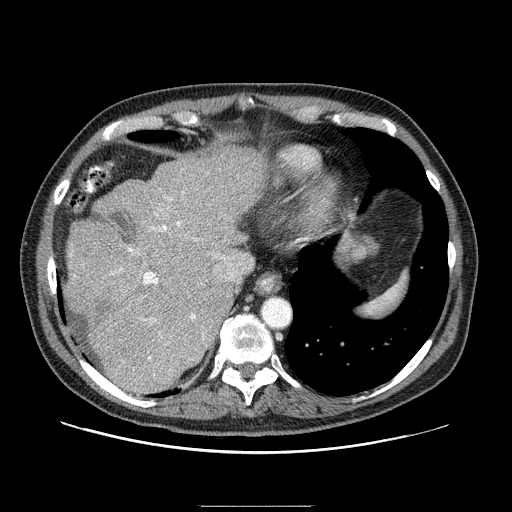
Contrast-enhanced abdominal CT (liver protocol), one axial slice; slice 69 of 99 in the series (ordered by position); reconstruction kernel STANDARD; one of 2 acquisitions stored at this slice position; soft-tissue window (W 400 / L 40 HU); 2.5 mm slice thickness; 512 × 512 image matrix, field of view 400 × 400 mm. Case-level facts recorded for this patient, not image findings: diagnosis: hepatocellular carcinoma (patient treated with transarterial chemoembolisation; whether this scan precedes or follows treatment is not stated here); TNM stage (as recorded): Stage-II; Child-Pugh class: A; tumour differentiation: well differentiated; tumour nodularity: multinodular.
Annotated regions visible in this slice (semi-automatically segmented with operator editing):
- abdominal aorta: bounding box [x1, y1, x2, y2] px = [262, 298, 290, 327]
- liver parenchyma outside the tumour (the mass and vessels are separate outlines, so this box may not span the whole liver): [62, 146, 265, 392]
- liver vessels: [111, 191, 223, 360]